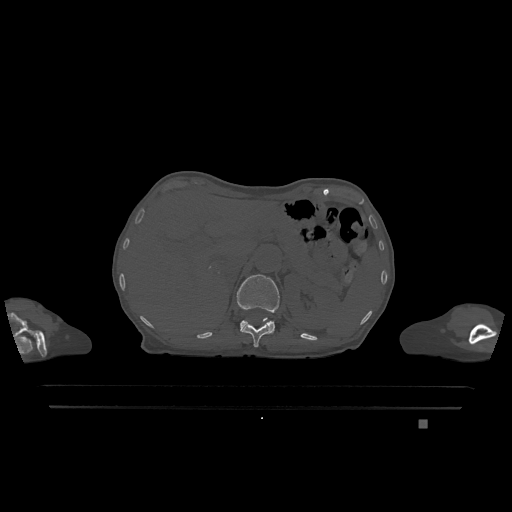
CT including the spine, one axial slice; position 504 of 1317 along the scan axis; bone window (W 1800 / L 400 HU); 512 × 512 image matrix, field of view 500 × 500 mm. Patient: female, 74 years. Case-level facts recorded for this patient, not image findings: primary cancer: lung.
Outlined on this slice (semi-automatic segmentation, software-assisted and operator-edited):
- L1 vertebra: box from (x=237, y=274) to (x=280, y=333) px
- T12 vertebra: (x=242, y=318)–(x=271, y=347)